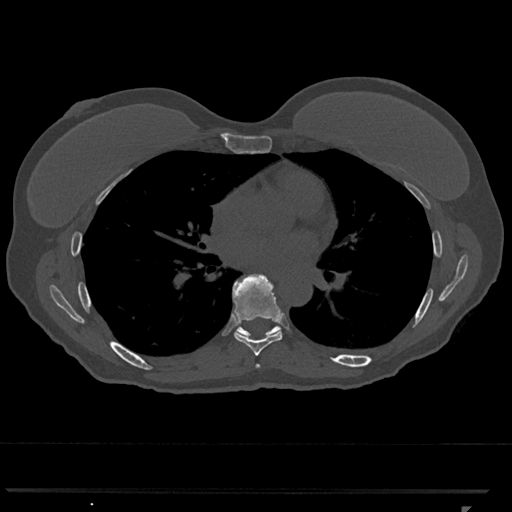
CT including the spine, one axial slice. Slice 701 of 793 in the series (ordered by position). 120 kVp. Bone window (W 1800 / L 400 HU). 0.5 mm slice thickness. 512 × 512 image matrix, field of view 380 × 380 mm. Female patient, age 62 years. Case-level facts recorded for this patient, not image findings: primary cancer: renal.
Structures marked on this image (semi-automatic segmentation, software-assisted and operator-edited):
- T6 vertebra: box from (x=256, y=364) to (x=260, y=368) px
- T7 vertebra: (x=233, y=274)–(x=283, y=356)
- T8 vertebra: (x=238, y=326)–(x=279, y=335)